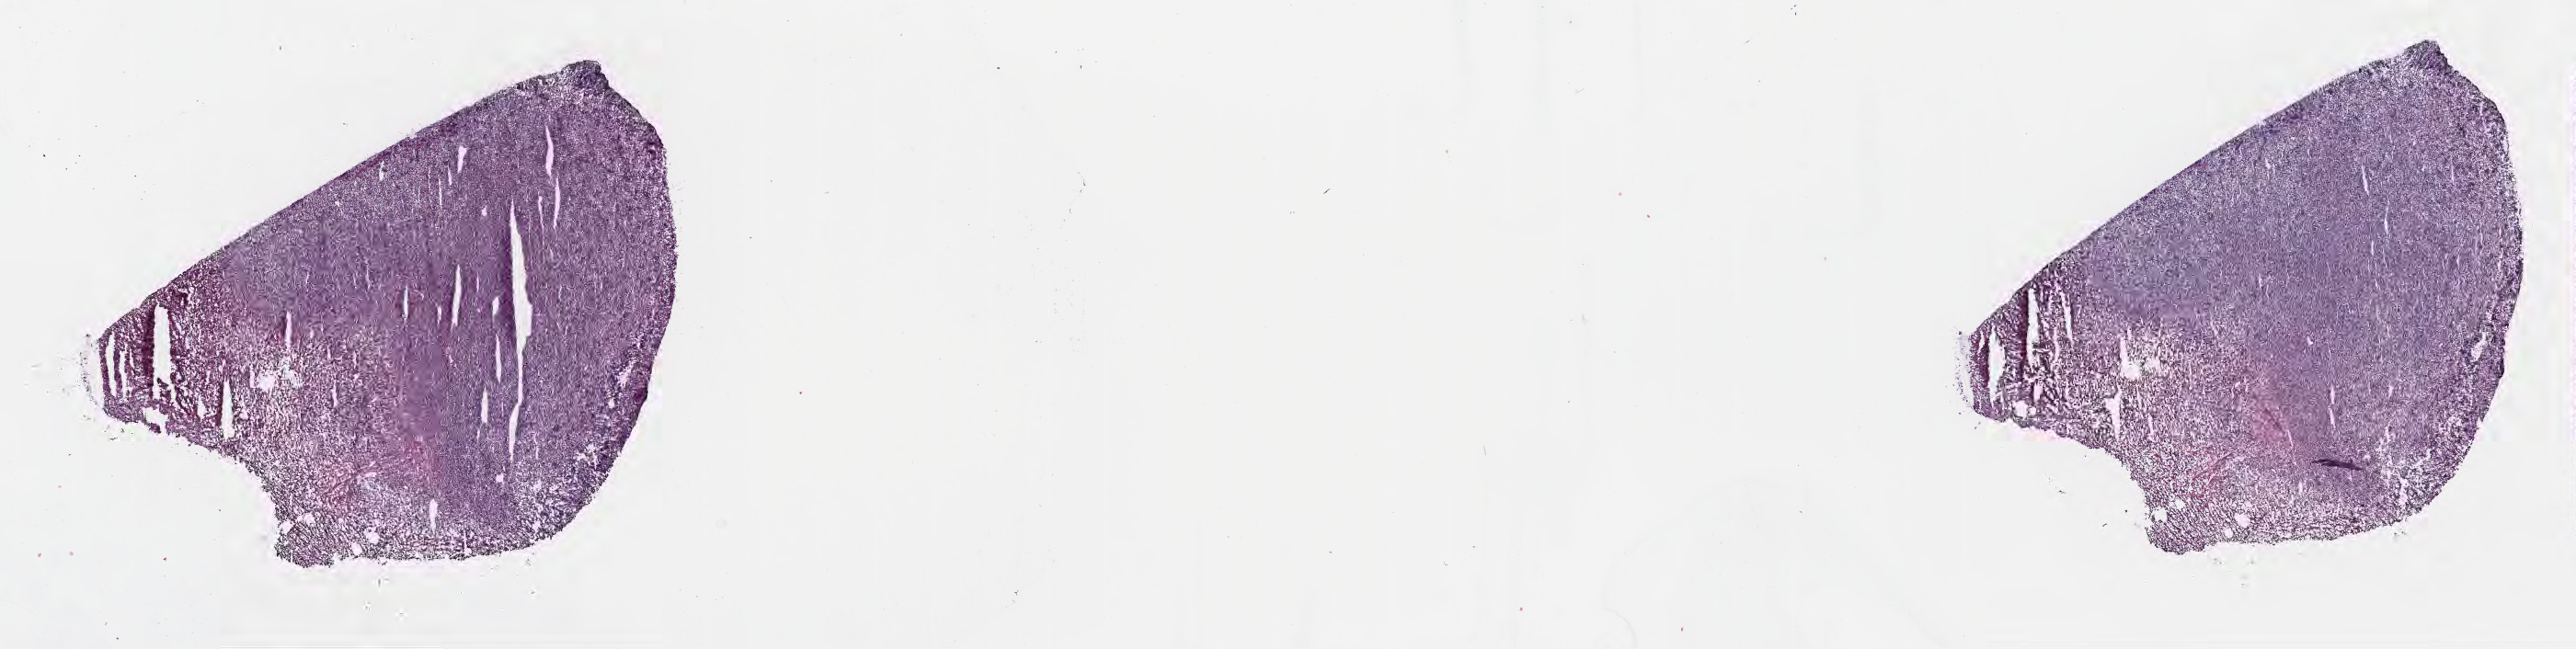
Whole-slide image, haematoxylin and eosin stain — a low-resolution overview of the entire scanned area, about 22.7 x 5.7 mm, cryosection, specimen: primary tumor, site: vestibule of mouth. Male patient; age at initial diagnosis 5 years. Pathologist review of this section (percent, as recorded): tumor cells 80%, tumor nuclei 90%.
Diagnosis: Diffuse large B-cell lymphoma, NOS.